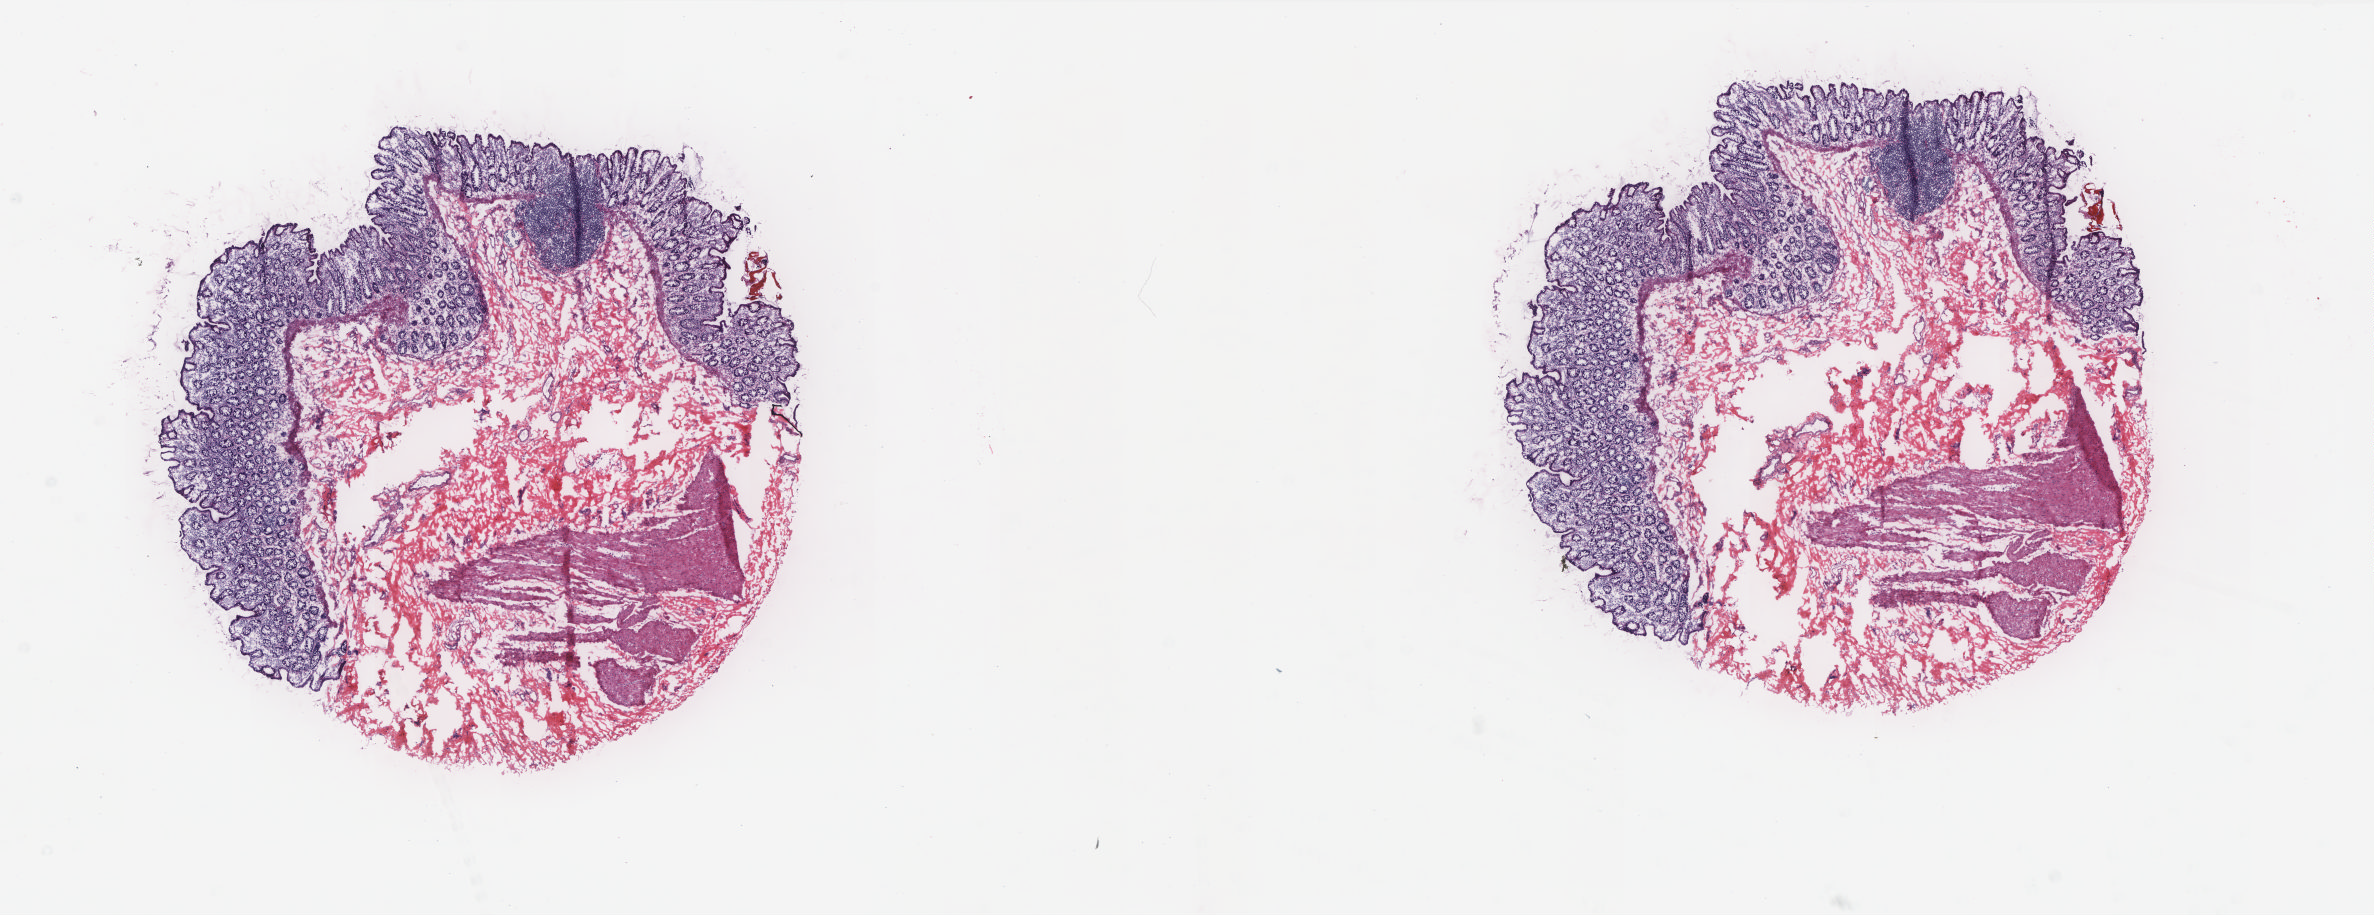
Whole-slide histology image, Hematoxylin and eosin (H&E) stained — low-resolution overview of the scanned area, about 19.0 x 7.3 mm (slide scanned at 20x); frozen section from the top of the tissue portion; colon, solid tissue normal (non-tumour tissue) sample. Male, age 68 years at initial diagnosis. Pathologist review of this section (percent, as recorded): tumour cells 0%, normal cells 100%. Inflammatory infiltration, as recorded: lymphocyte infiltration 50%, monocyte infiltration 10%, neutrophil infiltration 0%.
• this section: solid tissue normal sample (biorepository sample class)
• patient diagnosis: Adenocarcinoma, NOS